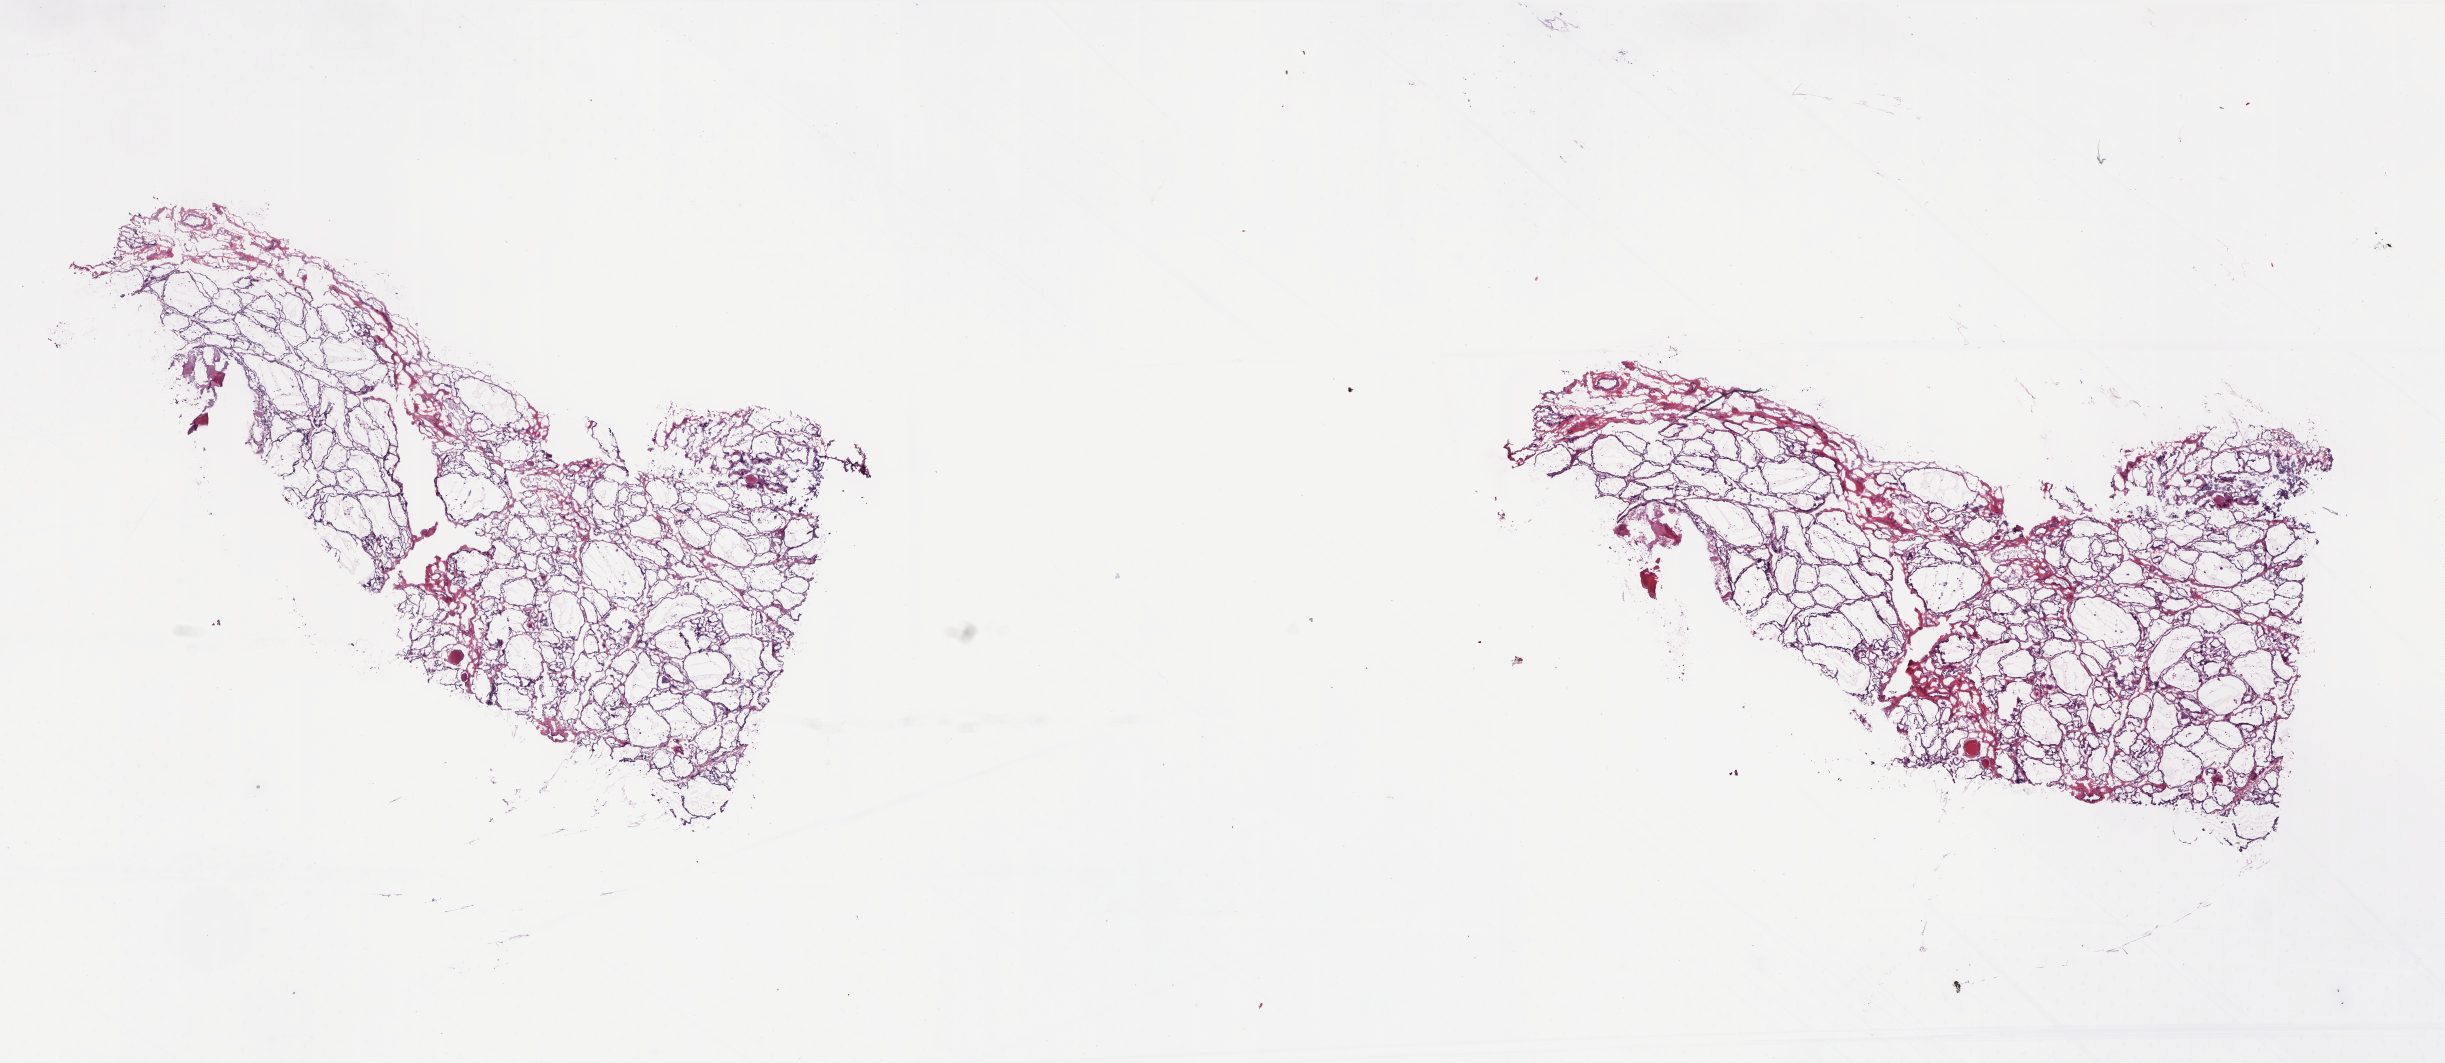
Digitized Hematoxylin and eosin (H&E) stained tissue section (whole slide), a low-resolution overview of the entire scanned area, about 19.7 x 8.6 mm; frozen section from the top of the tissue portion; sample: solid tissue normal (non-tumour tissue), thyroid. Patient: male, age at initial diagnosis 68 years. Composition of this section per pathologist review: tumour cells 0%, tumour nuclei 0%, normal cells 100%, stromal cells 0%, necrosis 0%. Inflammatory infiltration, as recorded: lymphocyte infiltration 1%, monocyte infiltration 2%, neutrophil infiltration 0%.
* this section: solid tissue normal (non-tumour) sample from the same patient
* patient diagnosis: Papillary adenocarcinoma, NOS (thyroid gland)